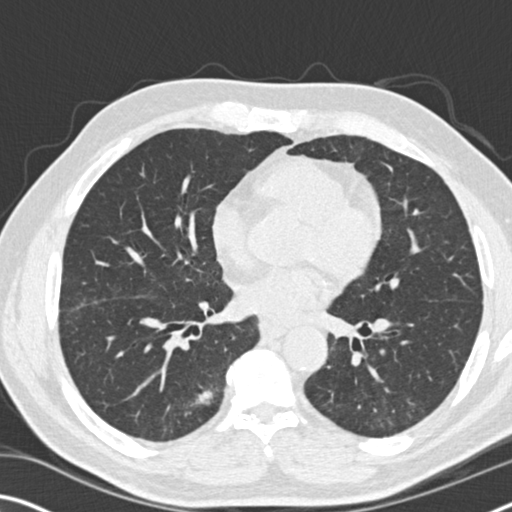
Low-dose screening chest CT, axial slice, first (baseline) screen, lung window (W 1500 / L -600 HU), 2 mm slice thickness, standard (soft-tissue) reconstruction kernel (B30f), slice 91 of 169 in the series. Male participant, aged 71 years at enrolment. Current smoker at enrolment.
Expert-annotated lung lesion, bounding box [x1, y1, x2, y2] px = [158, 374, 229, 434]. The screening reader recorded 2 non-calcified nodules or masses ≥4 mm on this exam (right lower lobe, left lower lobe); which of them this box marks is not recorded.